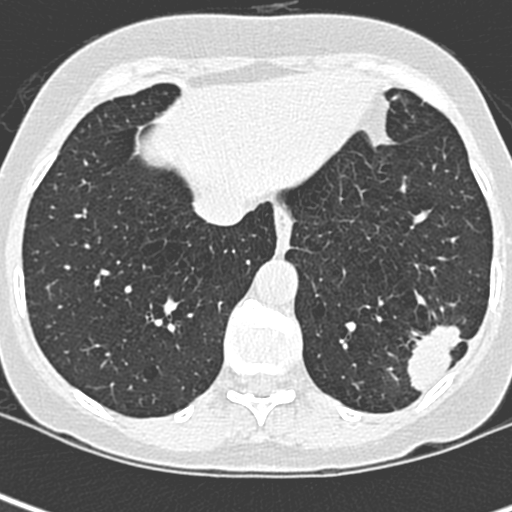
Low-dose screening chest CT, one axial slice; slice 75 of 252 in the series (ordered by position); lung window (W 1500 / L -600 HU); 512 × 512 image matrix, field of view 271 × 271 mm.
Outlined on this slice (manually delineated by an expert):
- lesion 1 (tumor, lower lobe of left lung): bounding box [x1, y1, x2, y2] px = [407, 325, 465, 394]